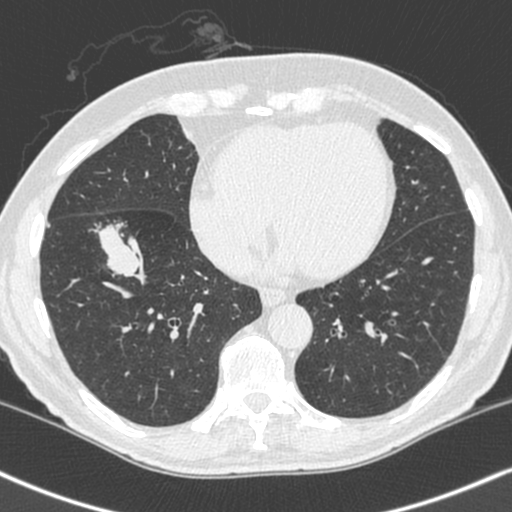
Chest CT (low-dose screening protocol), one axial image, baseline screening round, lung window (W 1500 / L -600 HU), 512 × 512 image matrix. Male participant, aged 68 years at enrolment. Current smoker at enrolment.
Expert-annotated lung lesion, bounding box [x1, y1, x2, y2] px = [82, 213, 157, 283]. The exam's reader record, not a measurement of the box and not confirmed to be the same lesion: non-calcified nodule or mass ≥4 mm, right lower lobe, 34 × 17 mm, smooth margins, soft tissue attenuation.